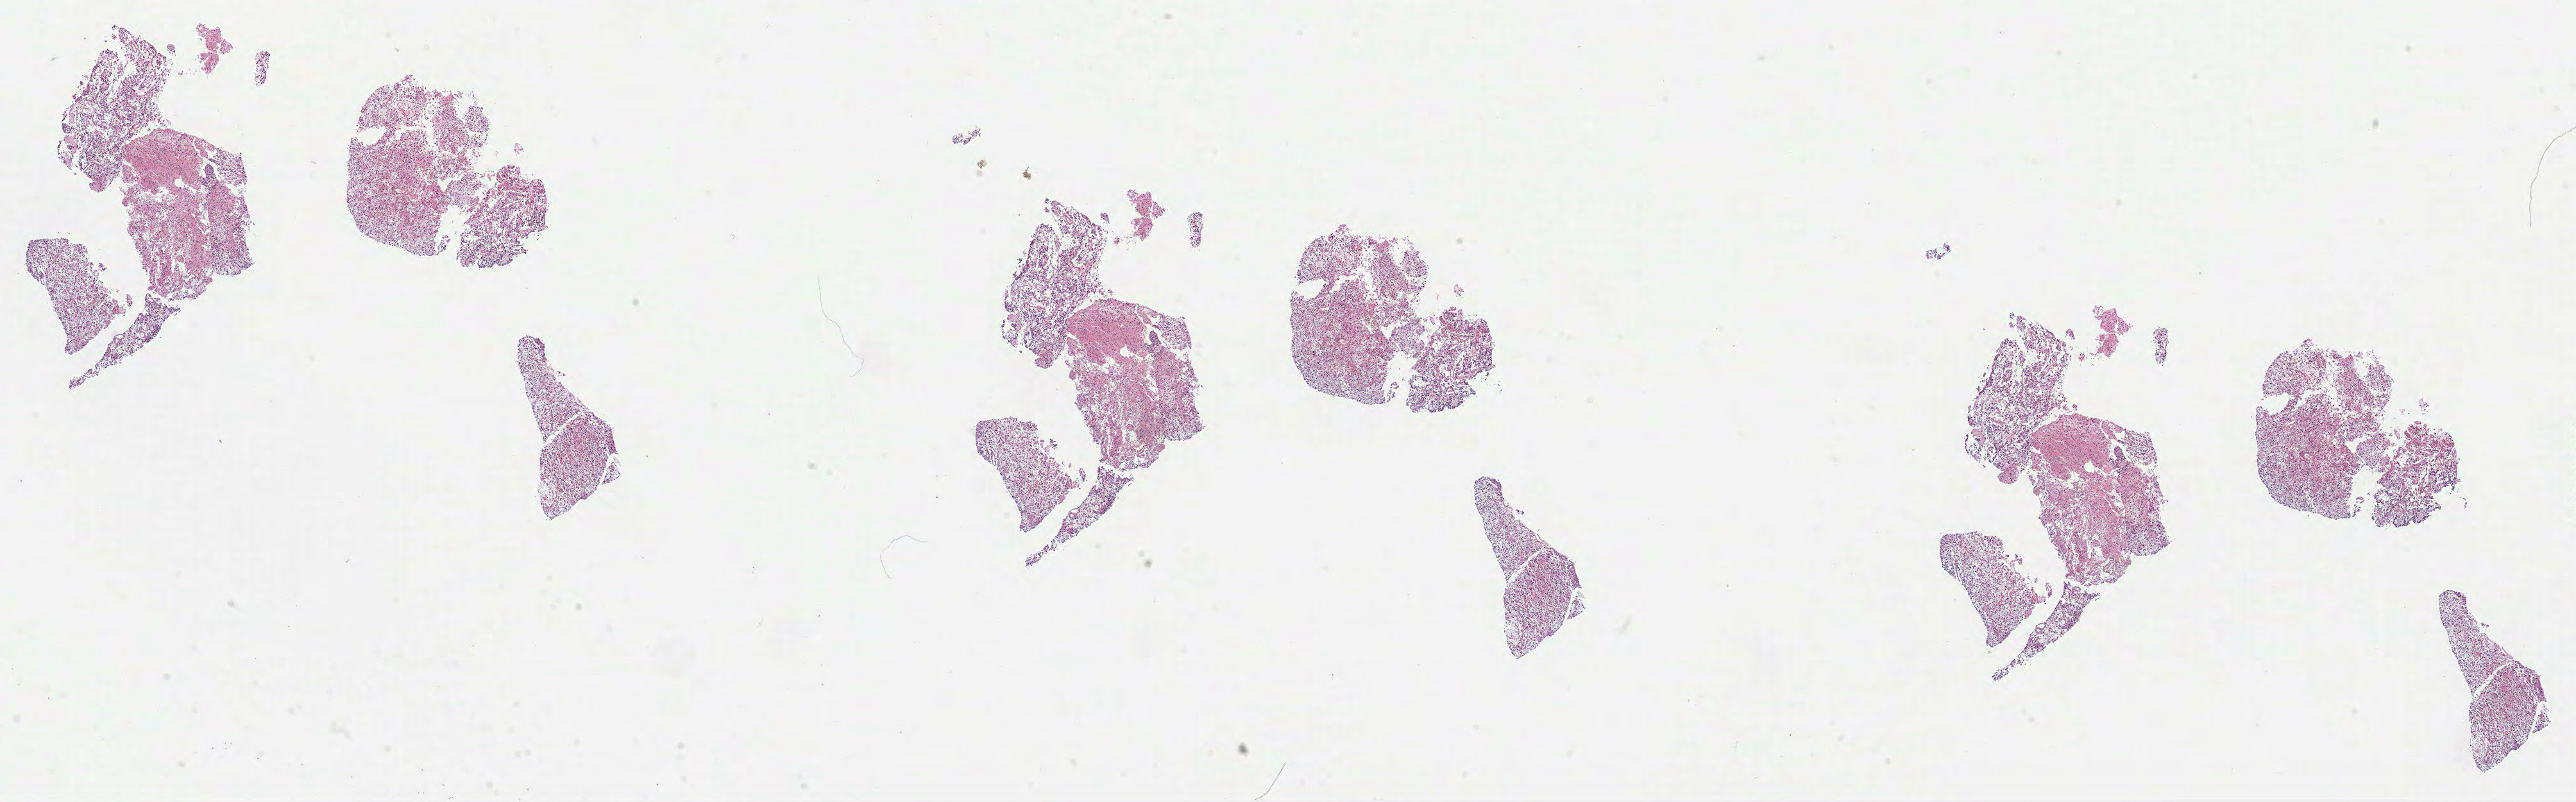
Whole-slide histology image, Hematoxylin and eosin (H&E) stained — a low-resolution overview of the entire scanned area, about 32.4 x 10.1 mm, formalin-fixed paraffin-embedded (FFPE) diagnostic section, sample: primary tumour, brain. Female, age 35 years at initial diagnosis. Histologic grade: G3 (poorly differentiated).
- laterality: right
- pathologic diagnosis: Astrocytoma, anaplastic (cerebrum)